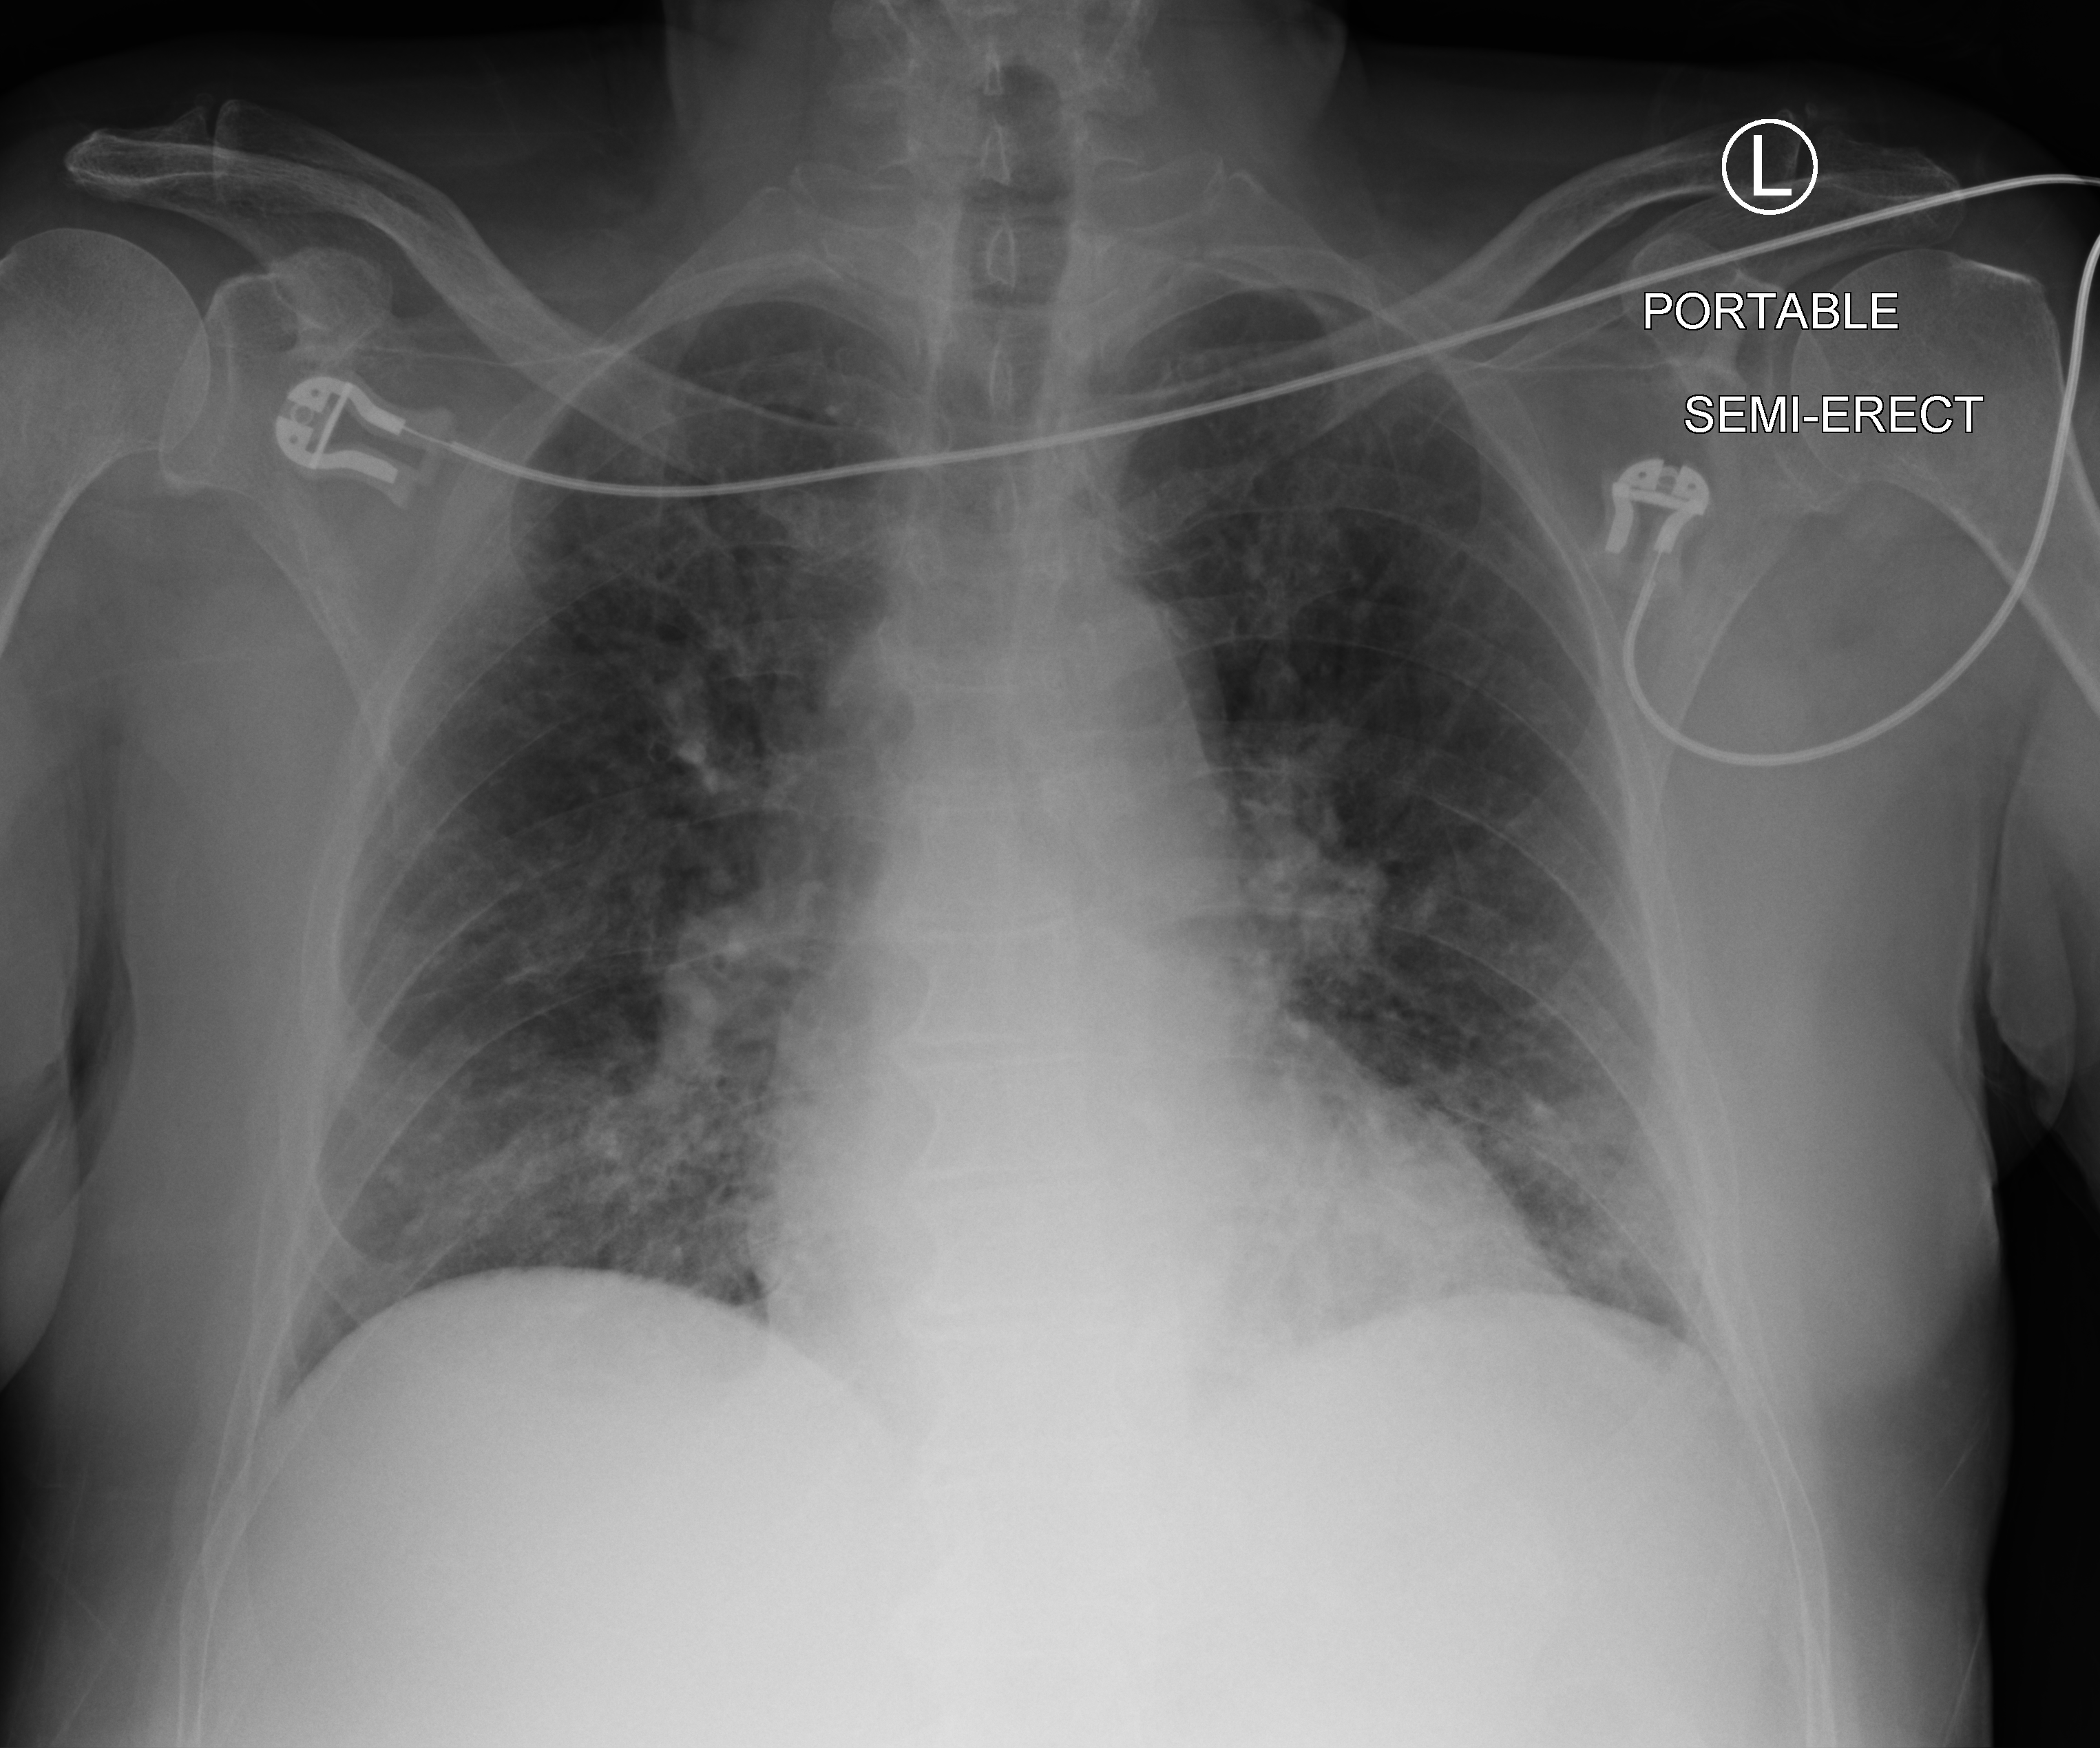
Chest X-ray (portable). Male patient hospitalised with COVID-19, age 75–90 years.
Admission-level facts for this patient (not findings on this image; timing relative to this image not recorded): length of hospital stay: 47 days; admitted to intensive care during this hospital stay: yes; mechanically ventilated during this hospital stay: yes.